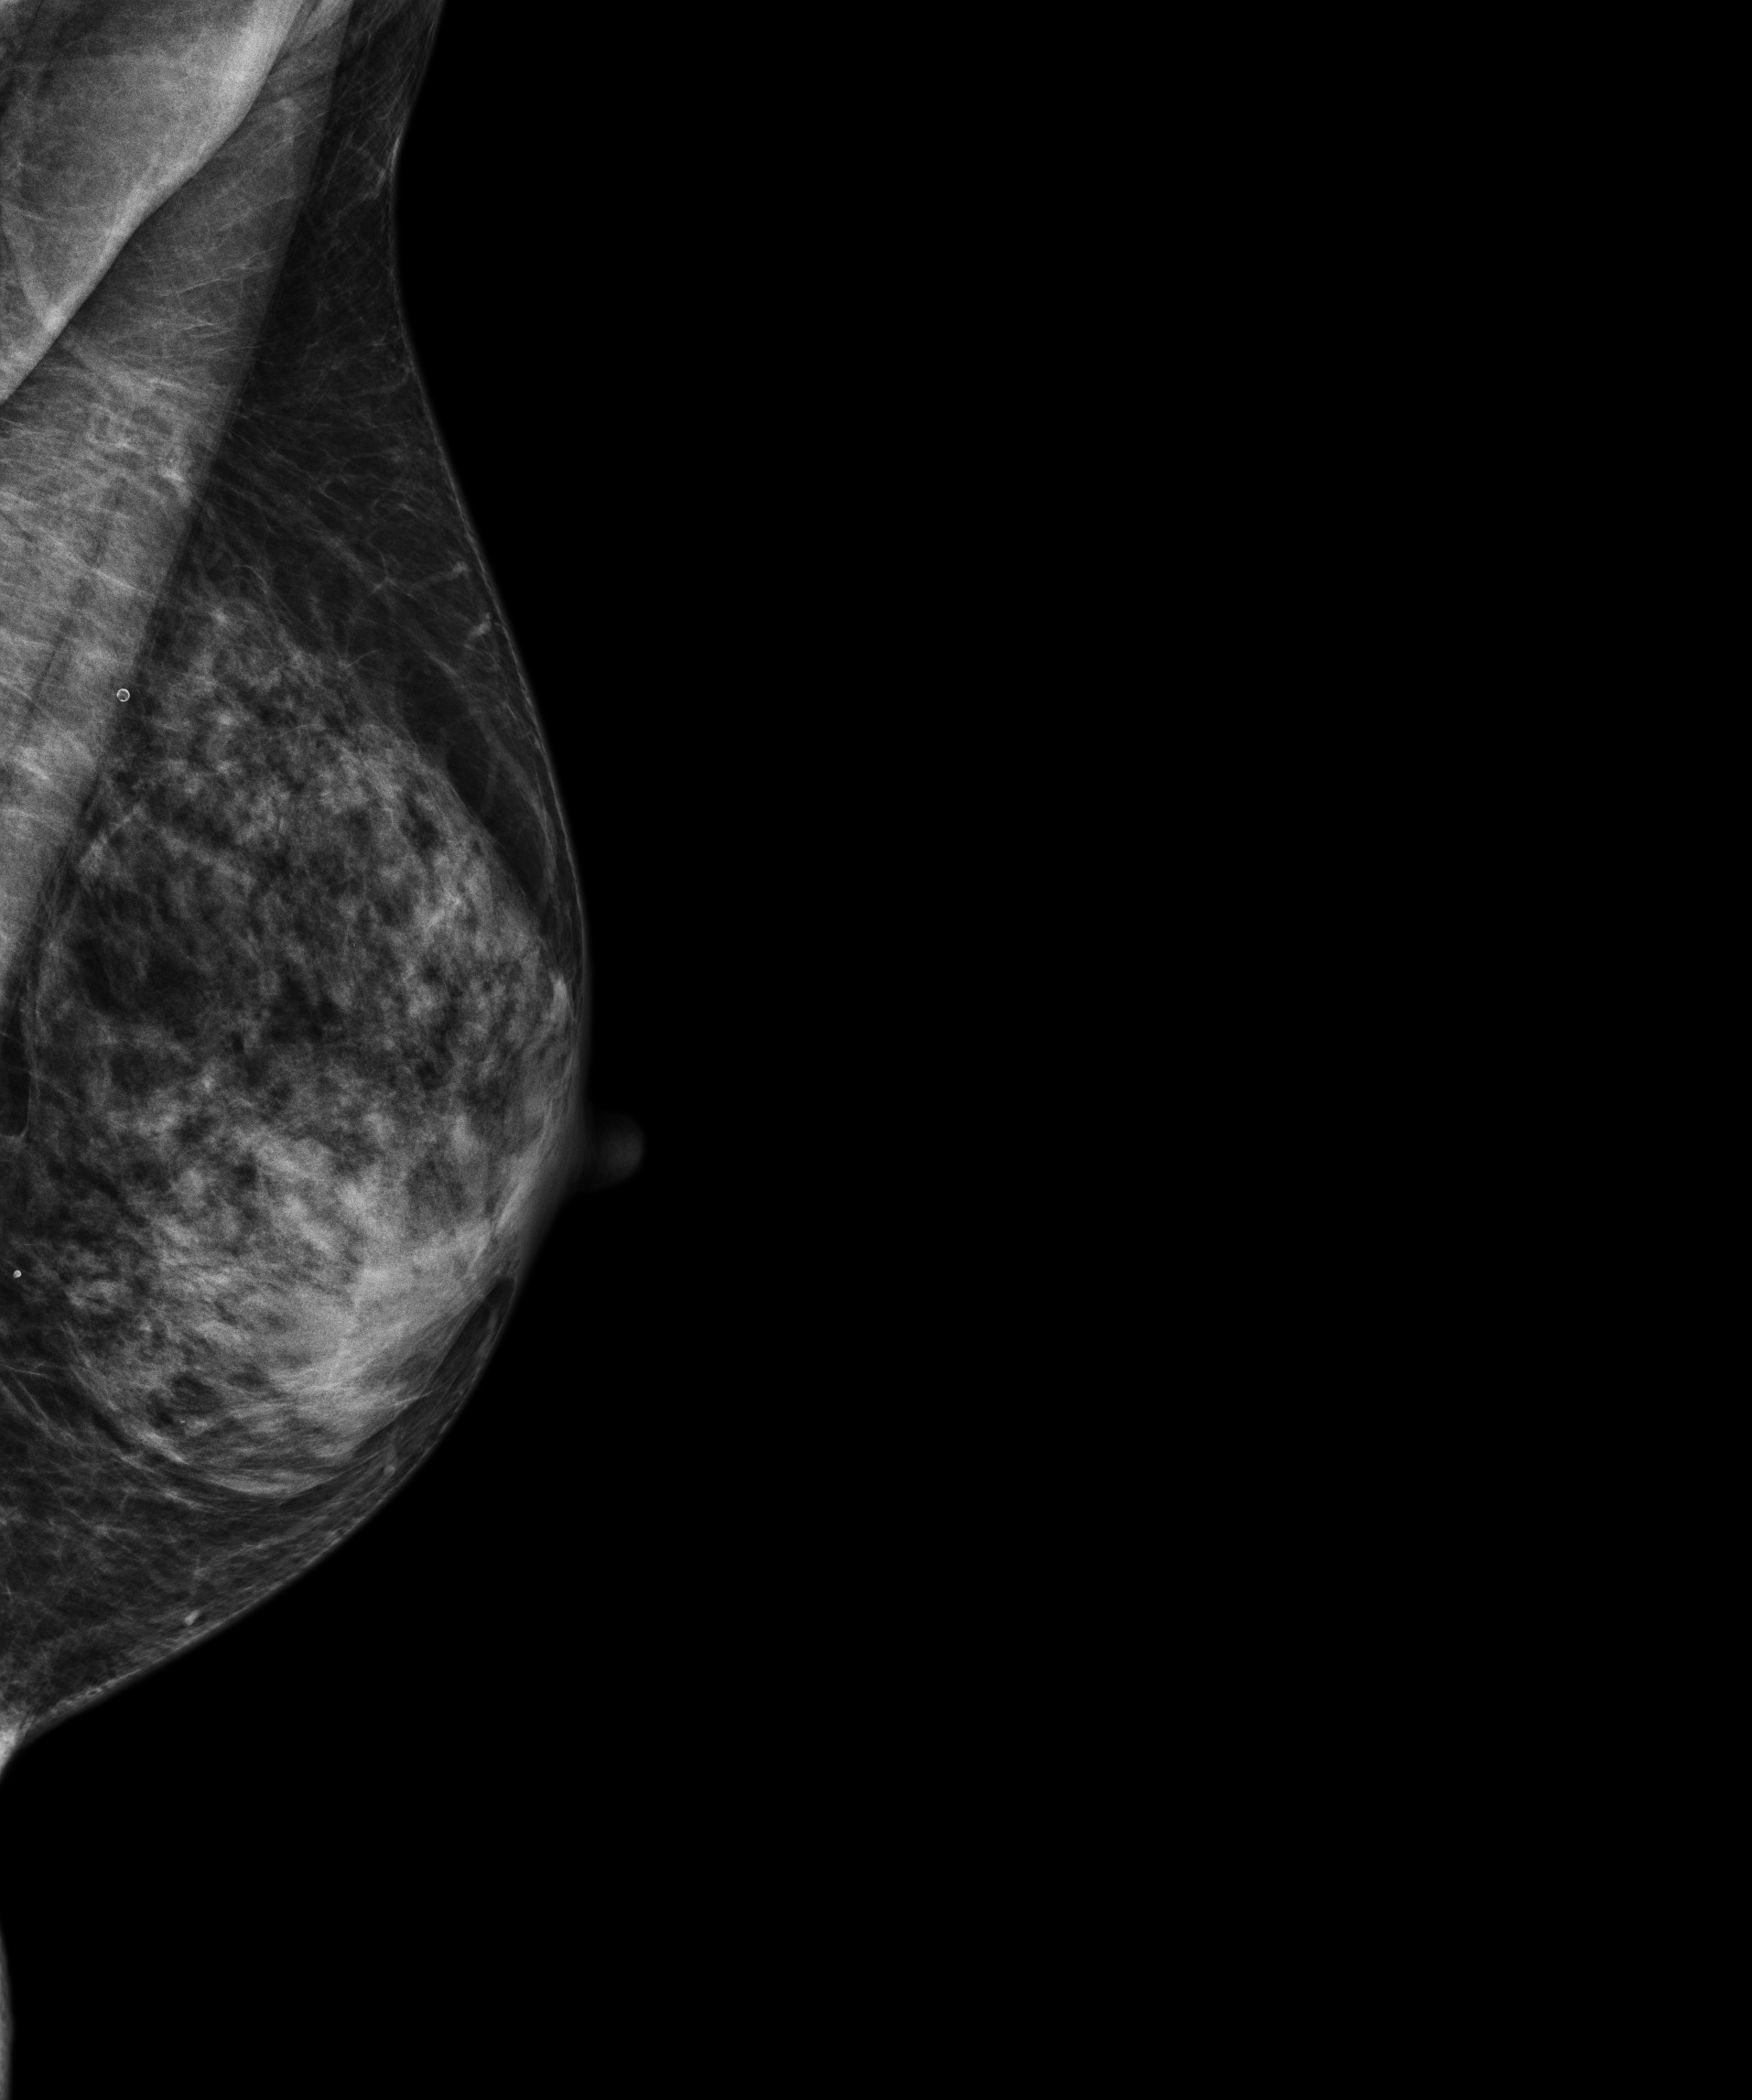
Digital mammogram (FFDM); left breast; mediolateral oblique (MLO) view; screening examination; compressed breast thickness 41 mm; system: Senographe Essential ADS_56.21.3. Patient aged 67 years (female).
- breast density at the screening exam (both breasts): heterogeneously dense (BI-RADS density category c)
- final BI-RADS category for the screening round (tomosynthesis exam, both breasts): category 1
- recall: no recall after this screen